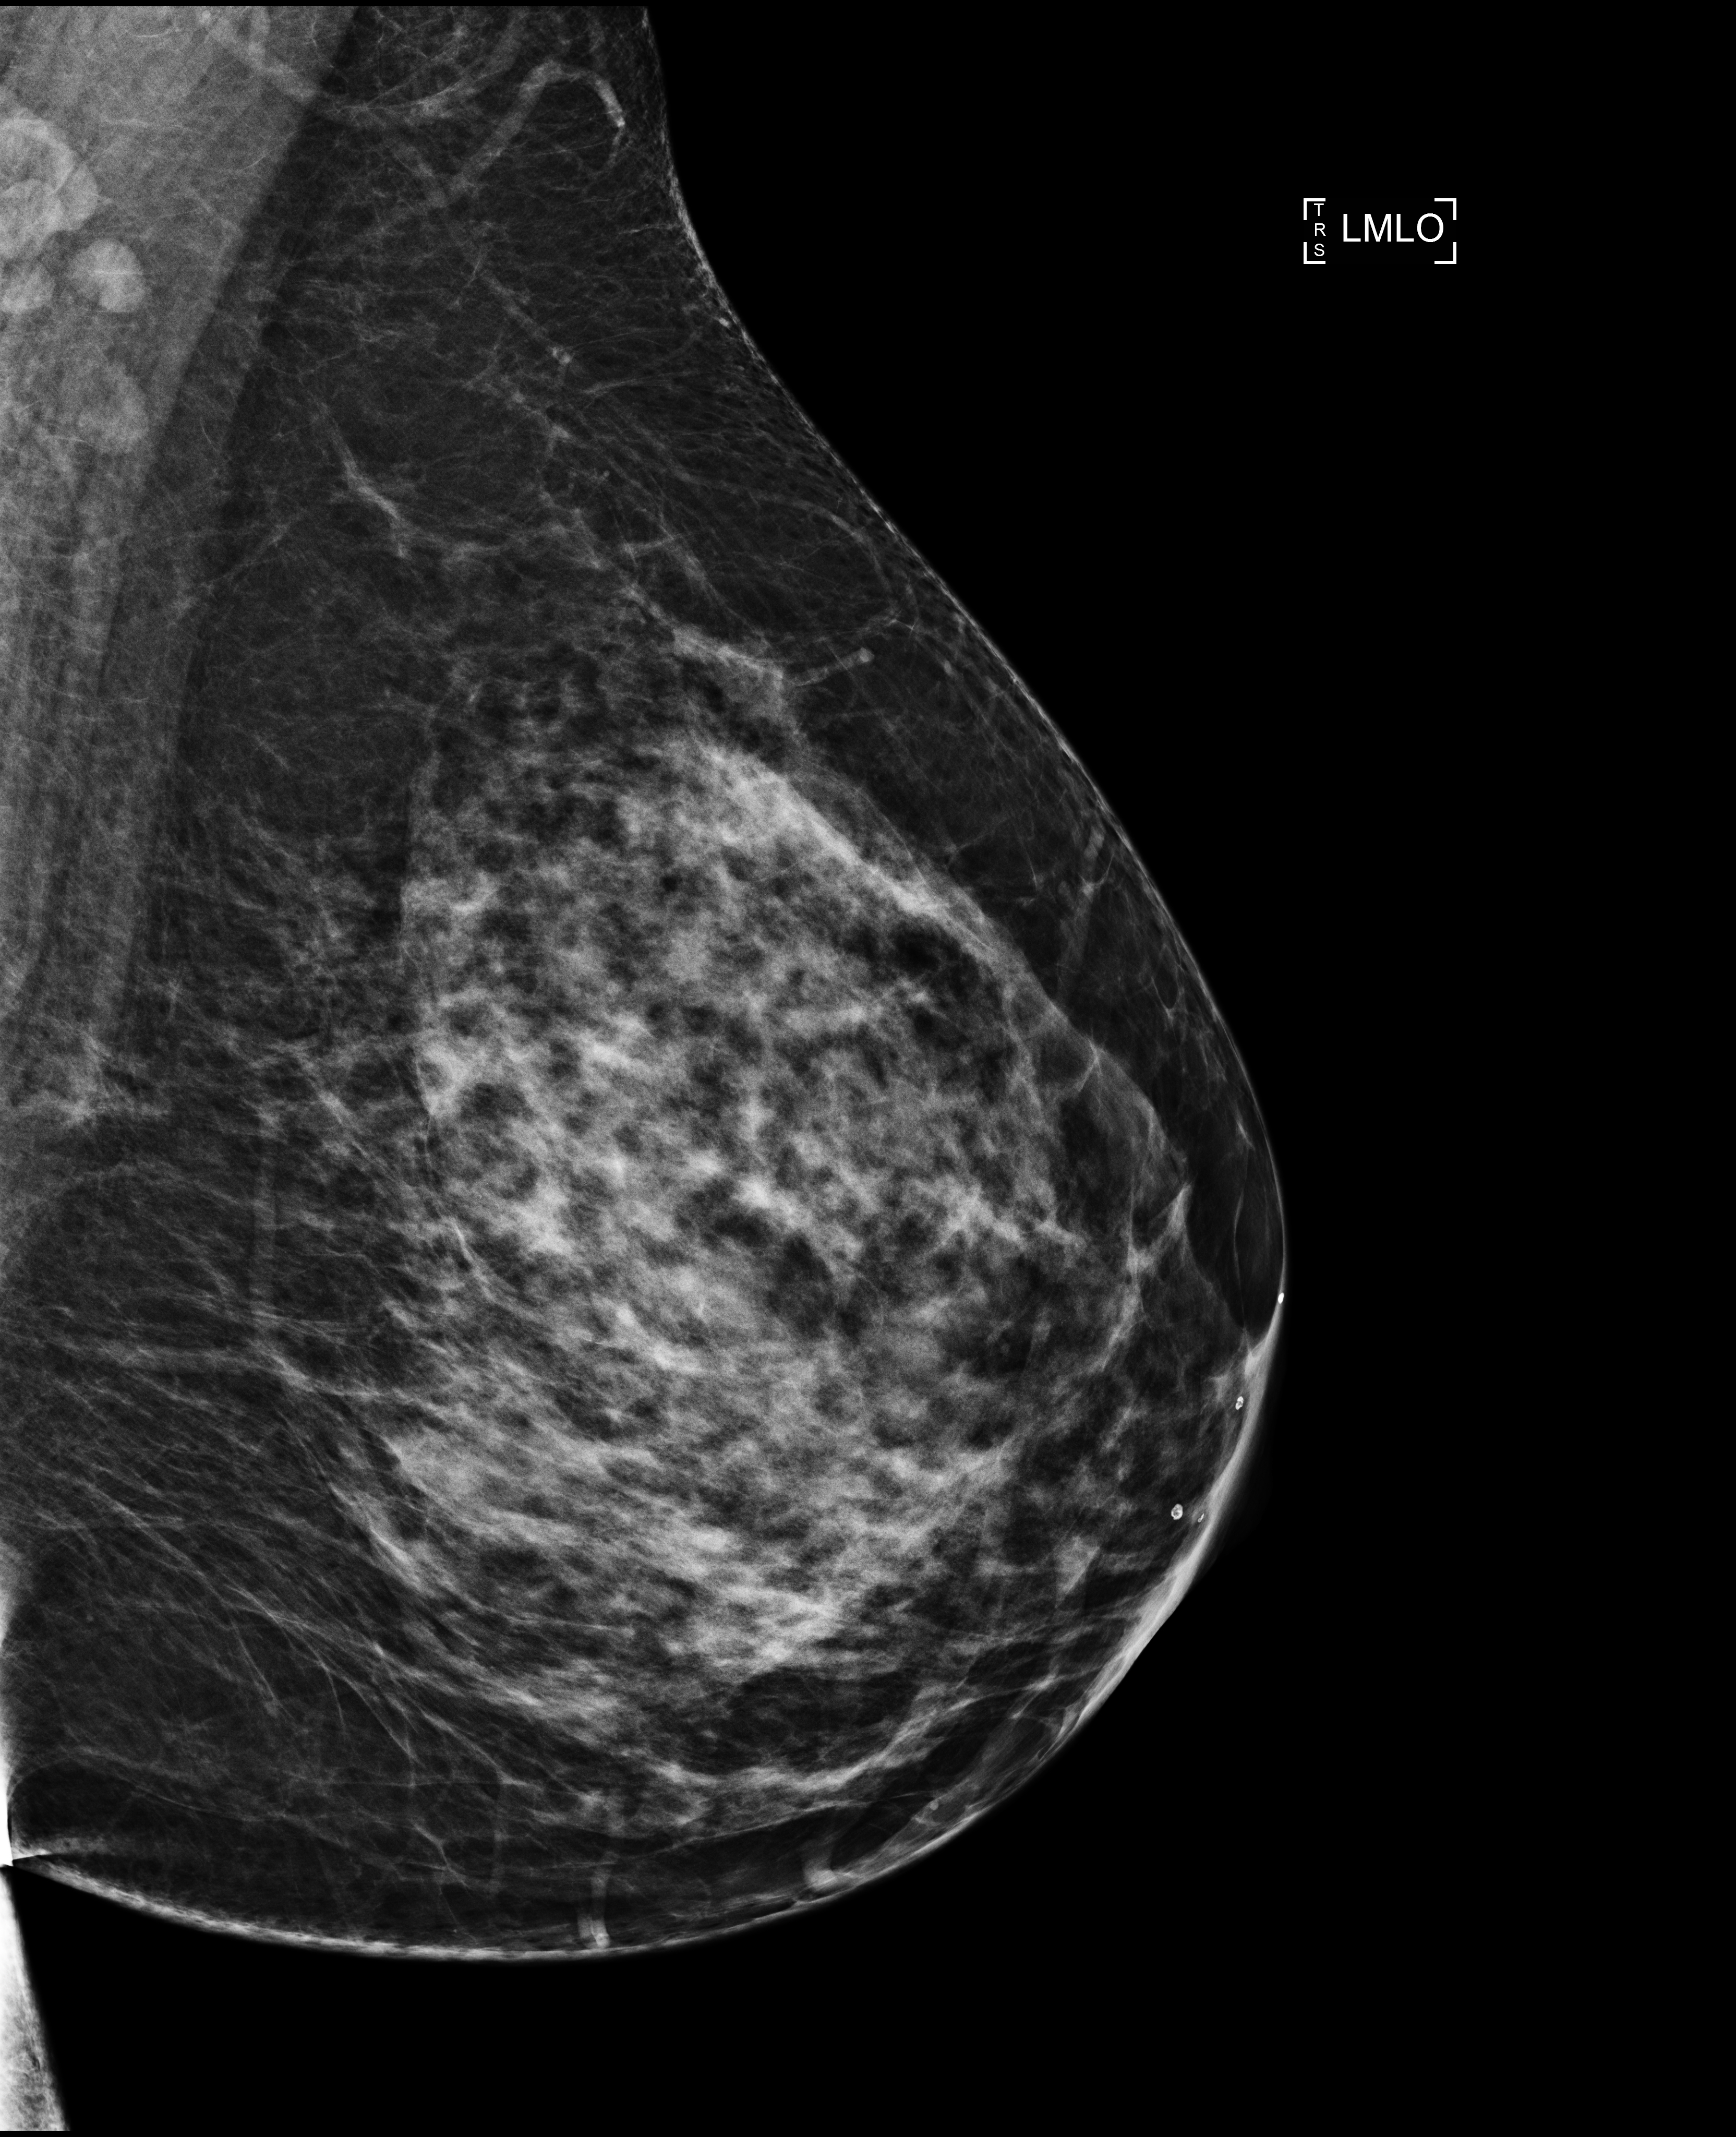
Screening examination; compressed breast thickness 86 mm. Female patient, age 45 years.
Image type: full-field digital mammogram. Breast: left. Projection: medio-lateral oblique projection.